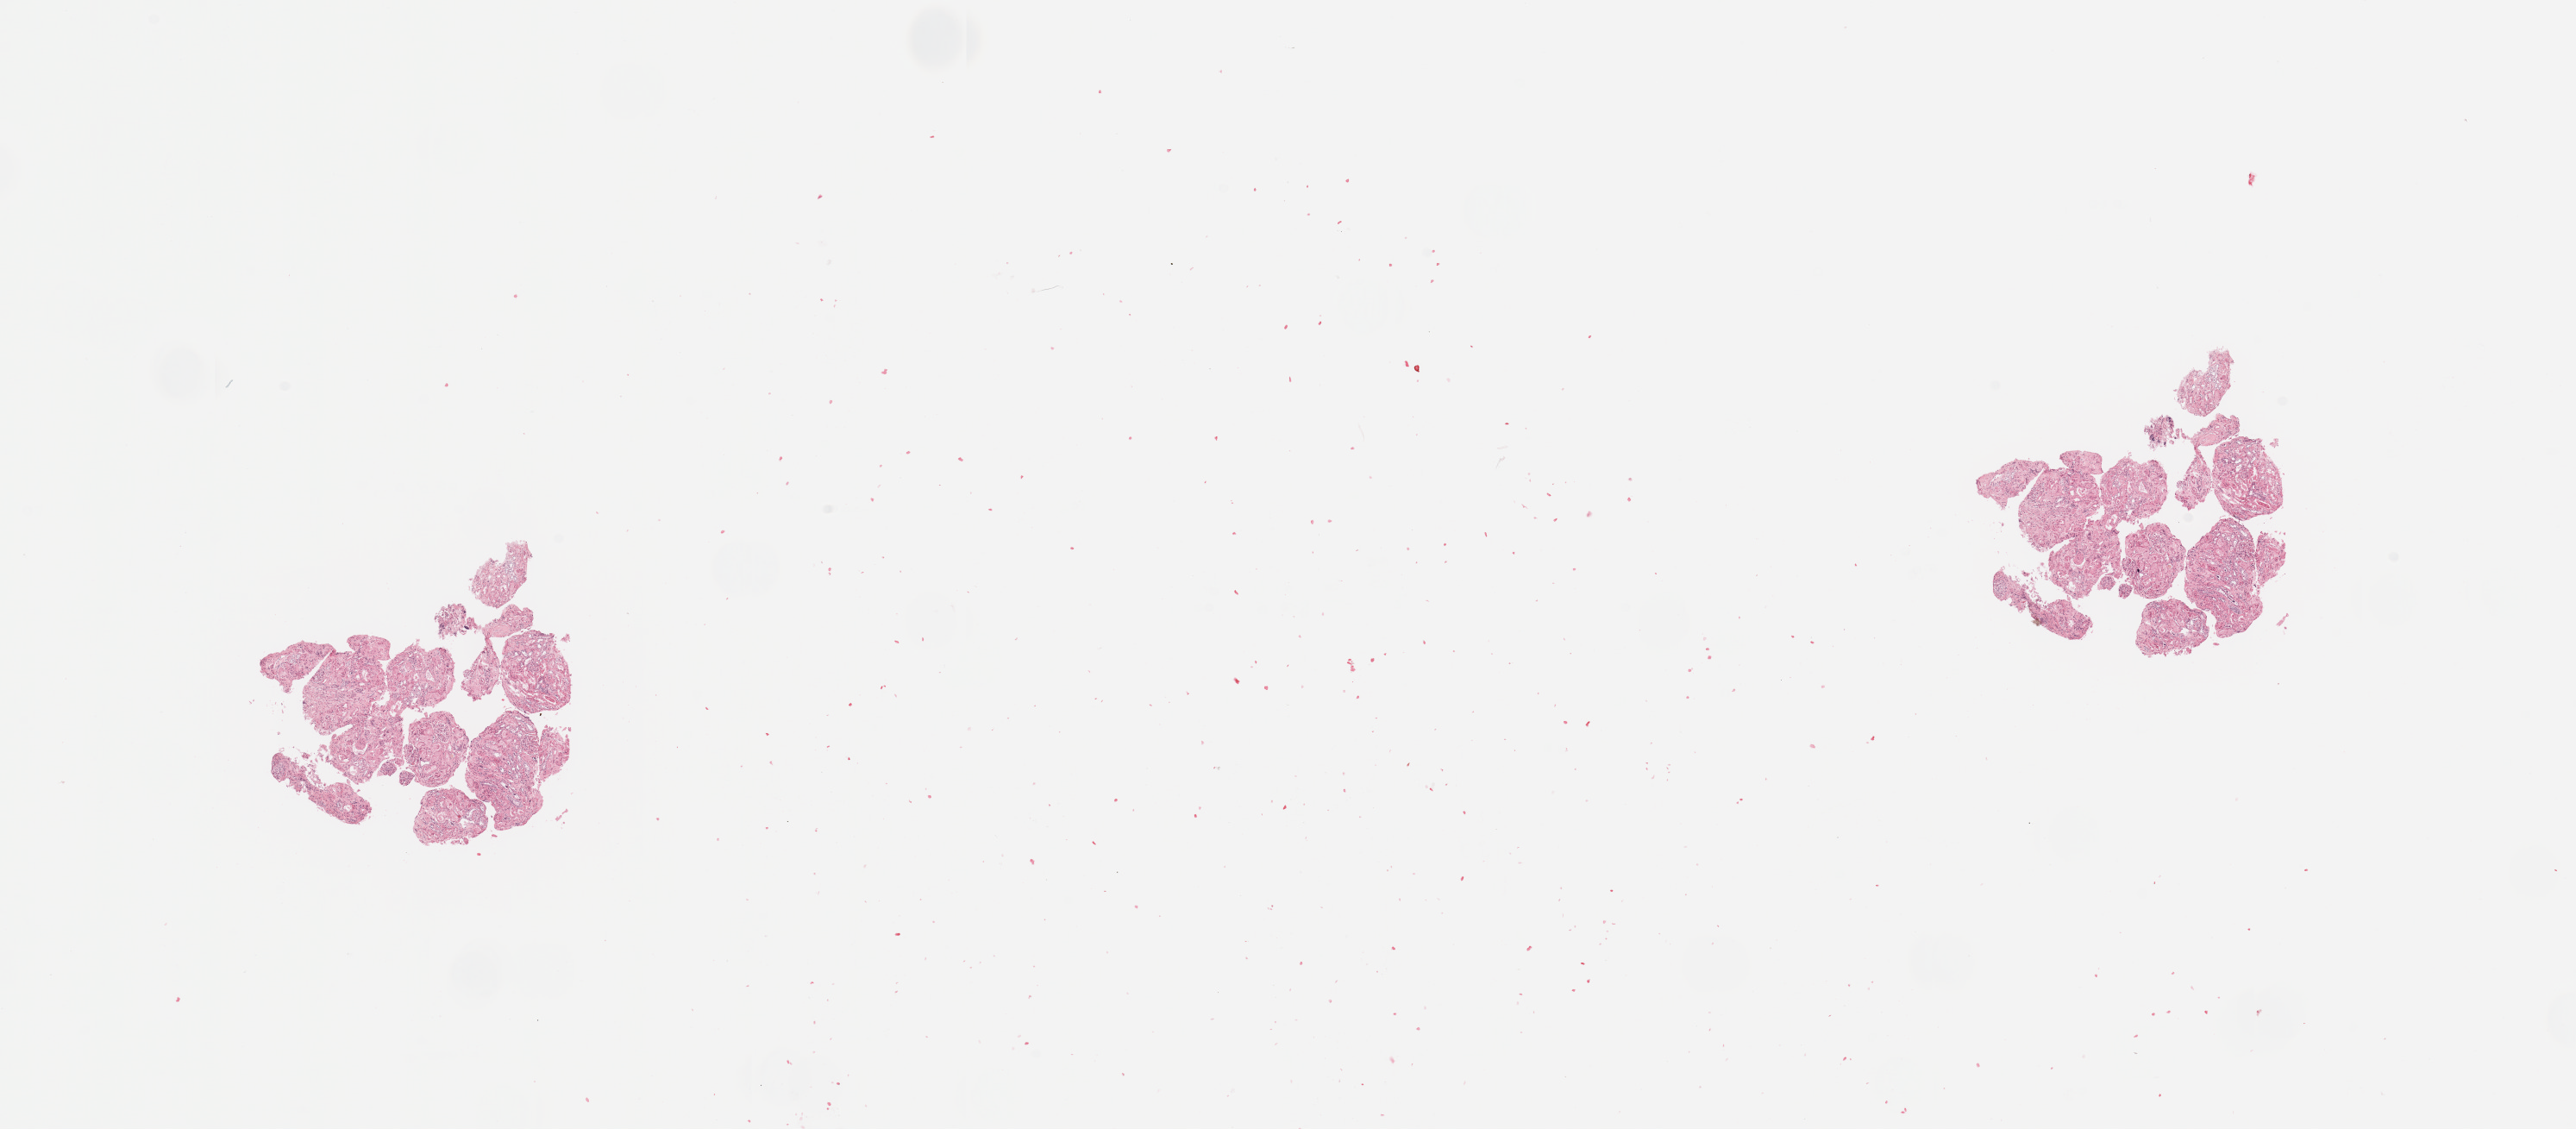
Hematoxylin and eosin (H&E) stained whole-slide image — a low-resolution overview of the entire scanned area, about 23.6 x 10.4 mm, kidney, normal (non-tumour) tissue. Male, 44 y/o.
- this section: normal (non-tumour) tissue from the same patient
- patient diagnosis: Renal cell carcinoma, NOS